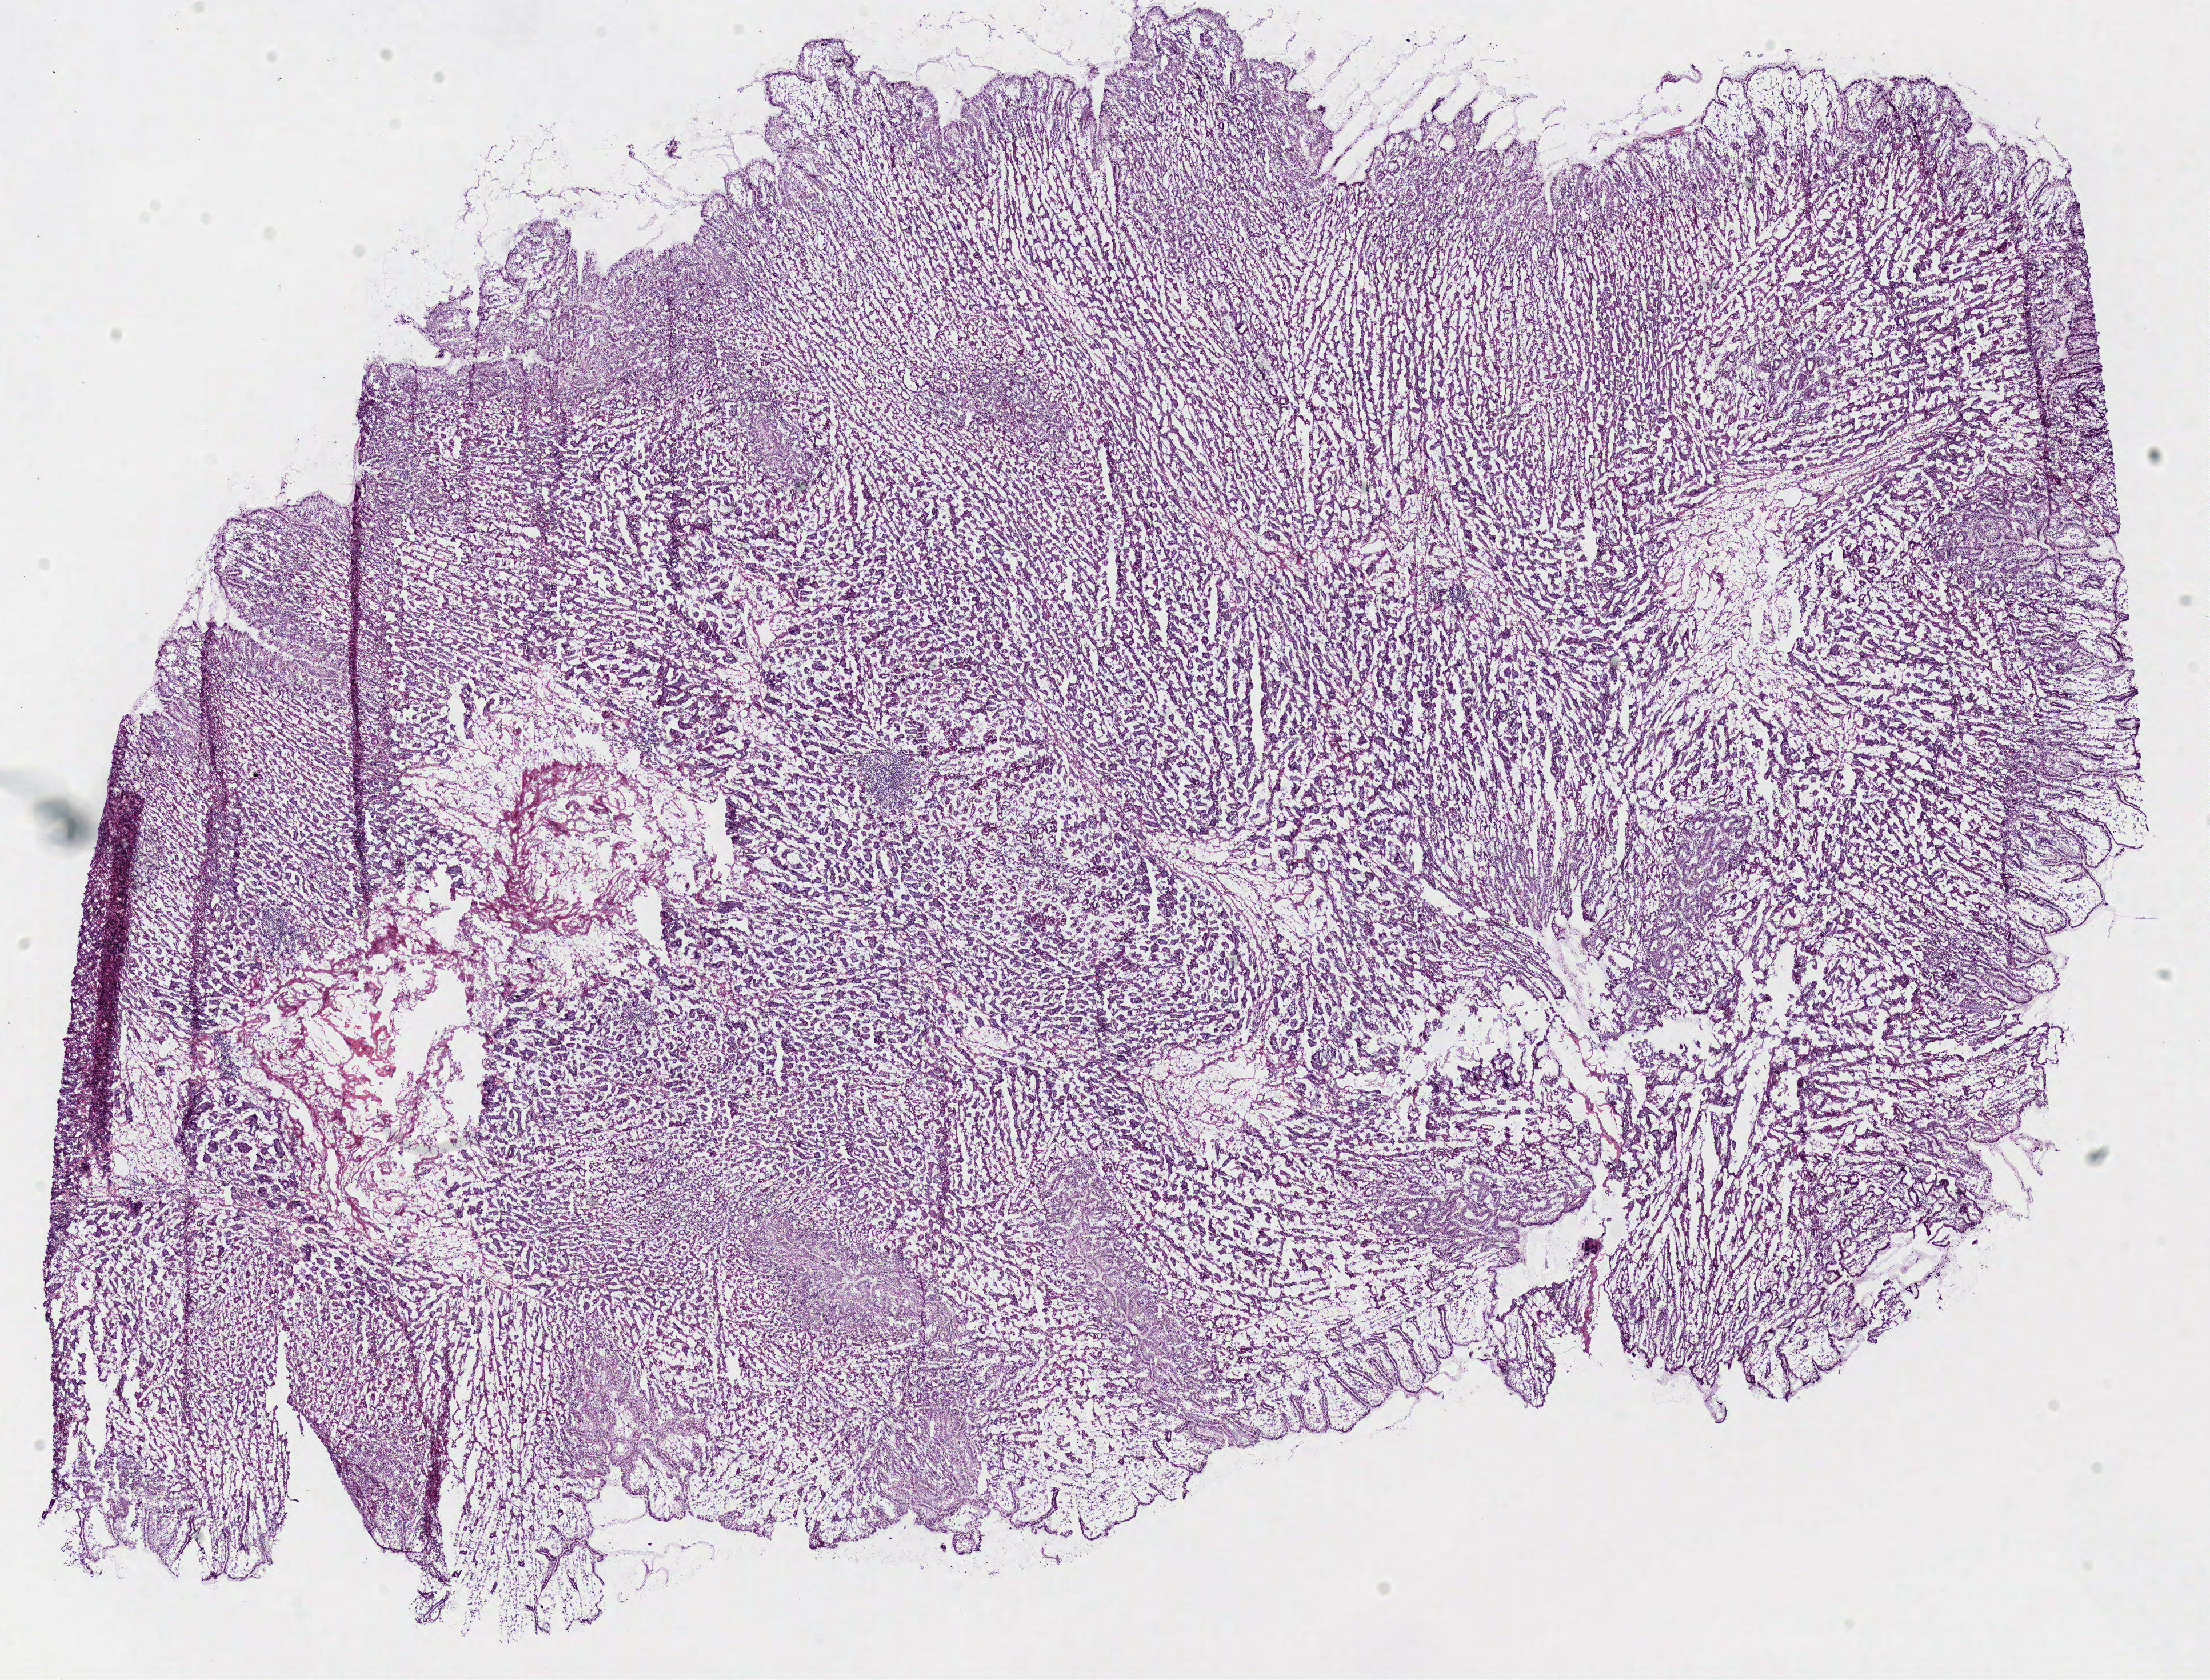
Hematoxylin and eosin (H&E) stained whole-slide image — a low-resolution overview of the entire scanned area, about 15.2 x 11.6 mm (from a 40x scan). Frozen section. Solid tissue normal (non-tumour tissue) sample from the stomach. Patient: female, age at initial diagnosis 57 years.
This section: solid tissue normal sample (biorepository sample class). Patient diagnosis: Adenocarcinoma, NOS.